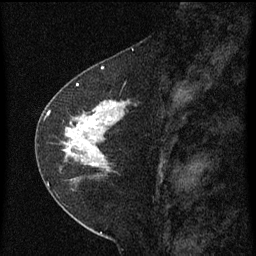
Breast MRI (dynamic contrast-enhanced), one sagittal slice; position 30 of 60 along the scan axis; dynamic contrast-enhanced series, image 2 of 3 at this slice position (ordered by acquisition); 1.5 T; TE 4.2 ms, TR 8 ms; 2 mm slice thickness; 256 × 256 image matrix, field of view 180 × 180 mm. Female patient, age 47 years.
Annotated regions visible in this slice (semi-automatically segmented with operator editing):
- analysis volume of interest (the breast-tissue region the enhancement analysis was run in; not a lesion): bounding box [x1, y1, x2, y2] px = [44, 84, 139, 199]
- tumour enhancement mask (voxels above the 70 % enhancement threshold inside the analysis volume of interest): [44, 84, 125, 185]